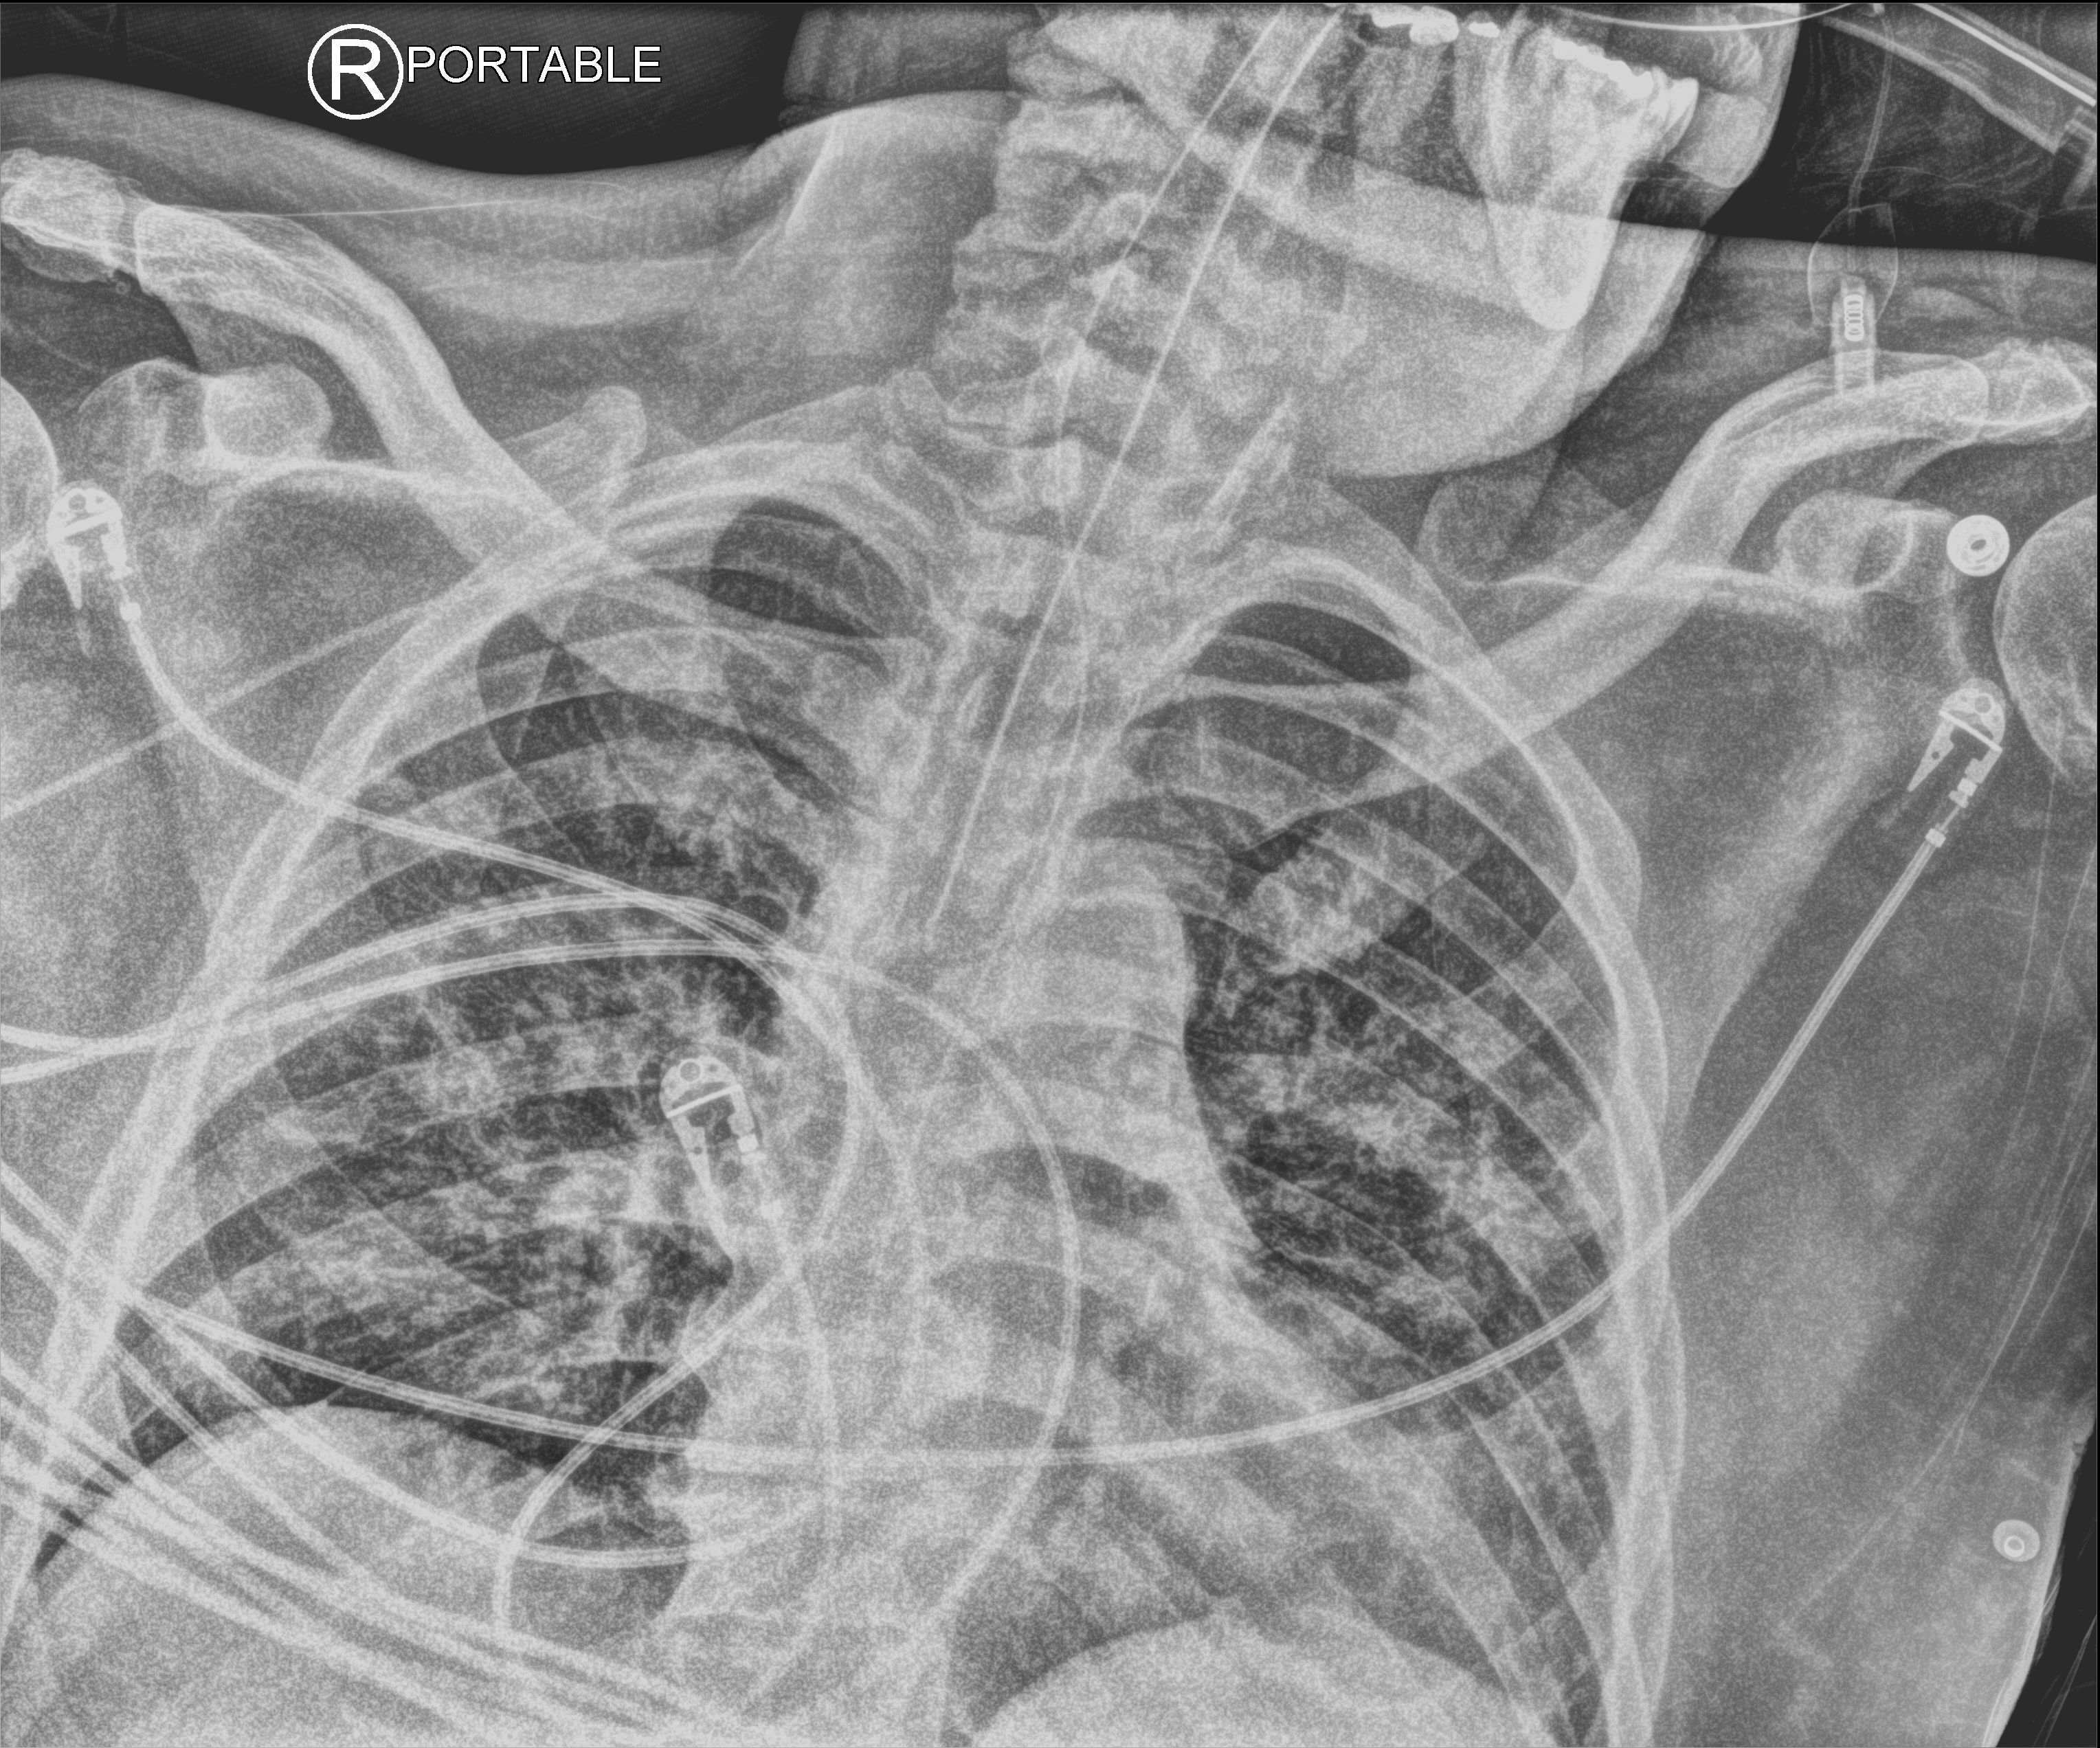
Chest X-ray (portable); anteroposterior (AP) projection. Male patient hospitalised with COVID-19, age 18–59 years.
Admission-level facts for this patient (not findings on this image; timing relative to this image not recorded):
- smoking status (admission record): never
- chronic kidney disease (admission record): no